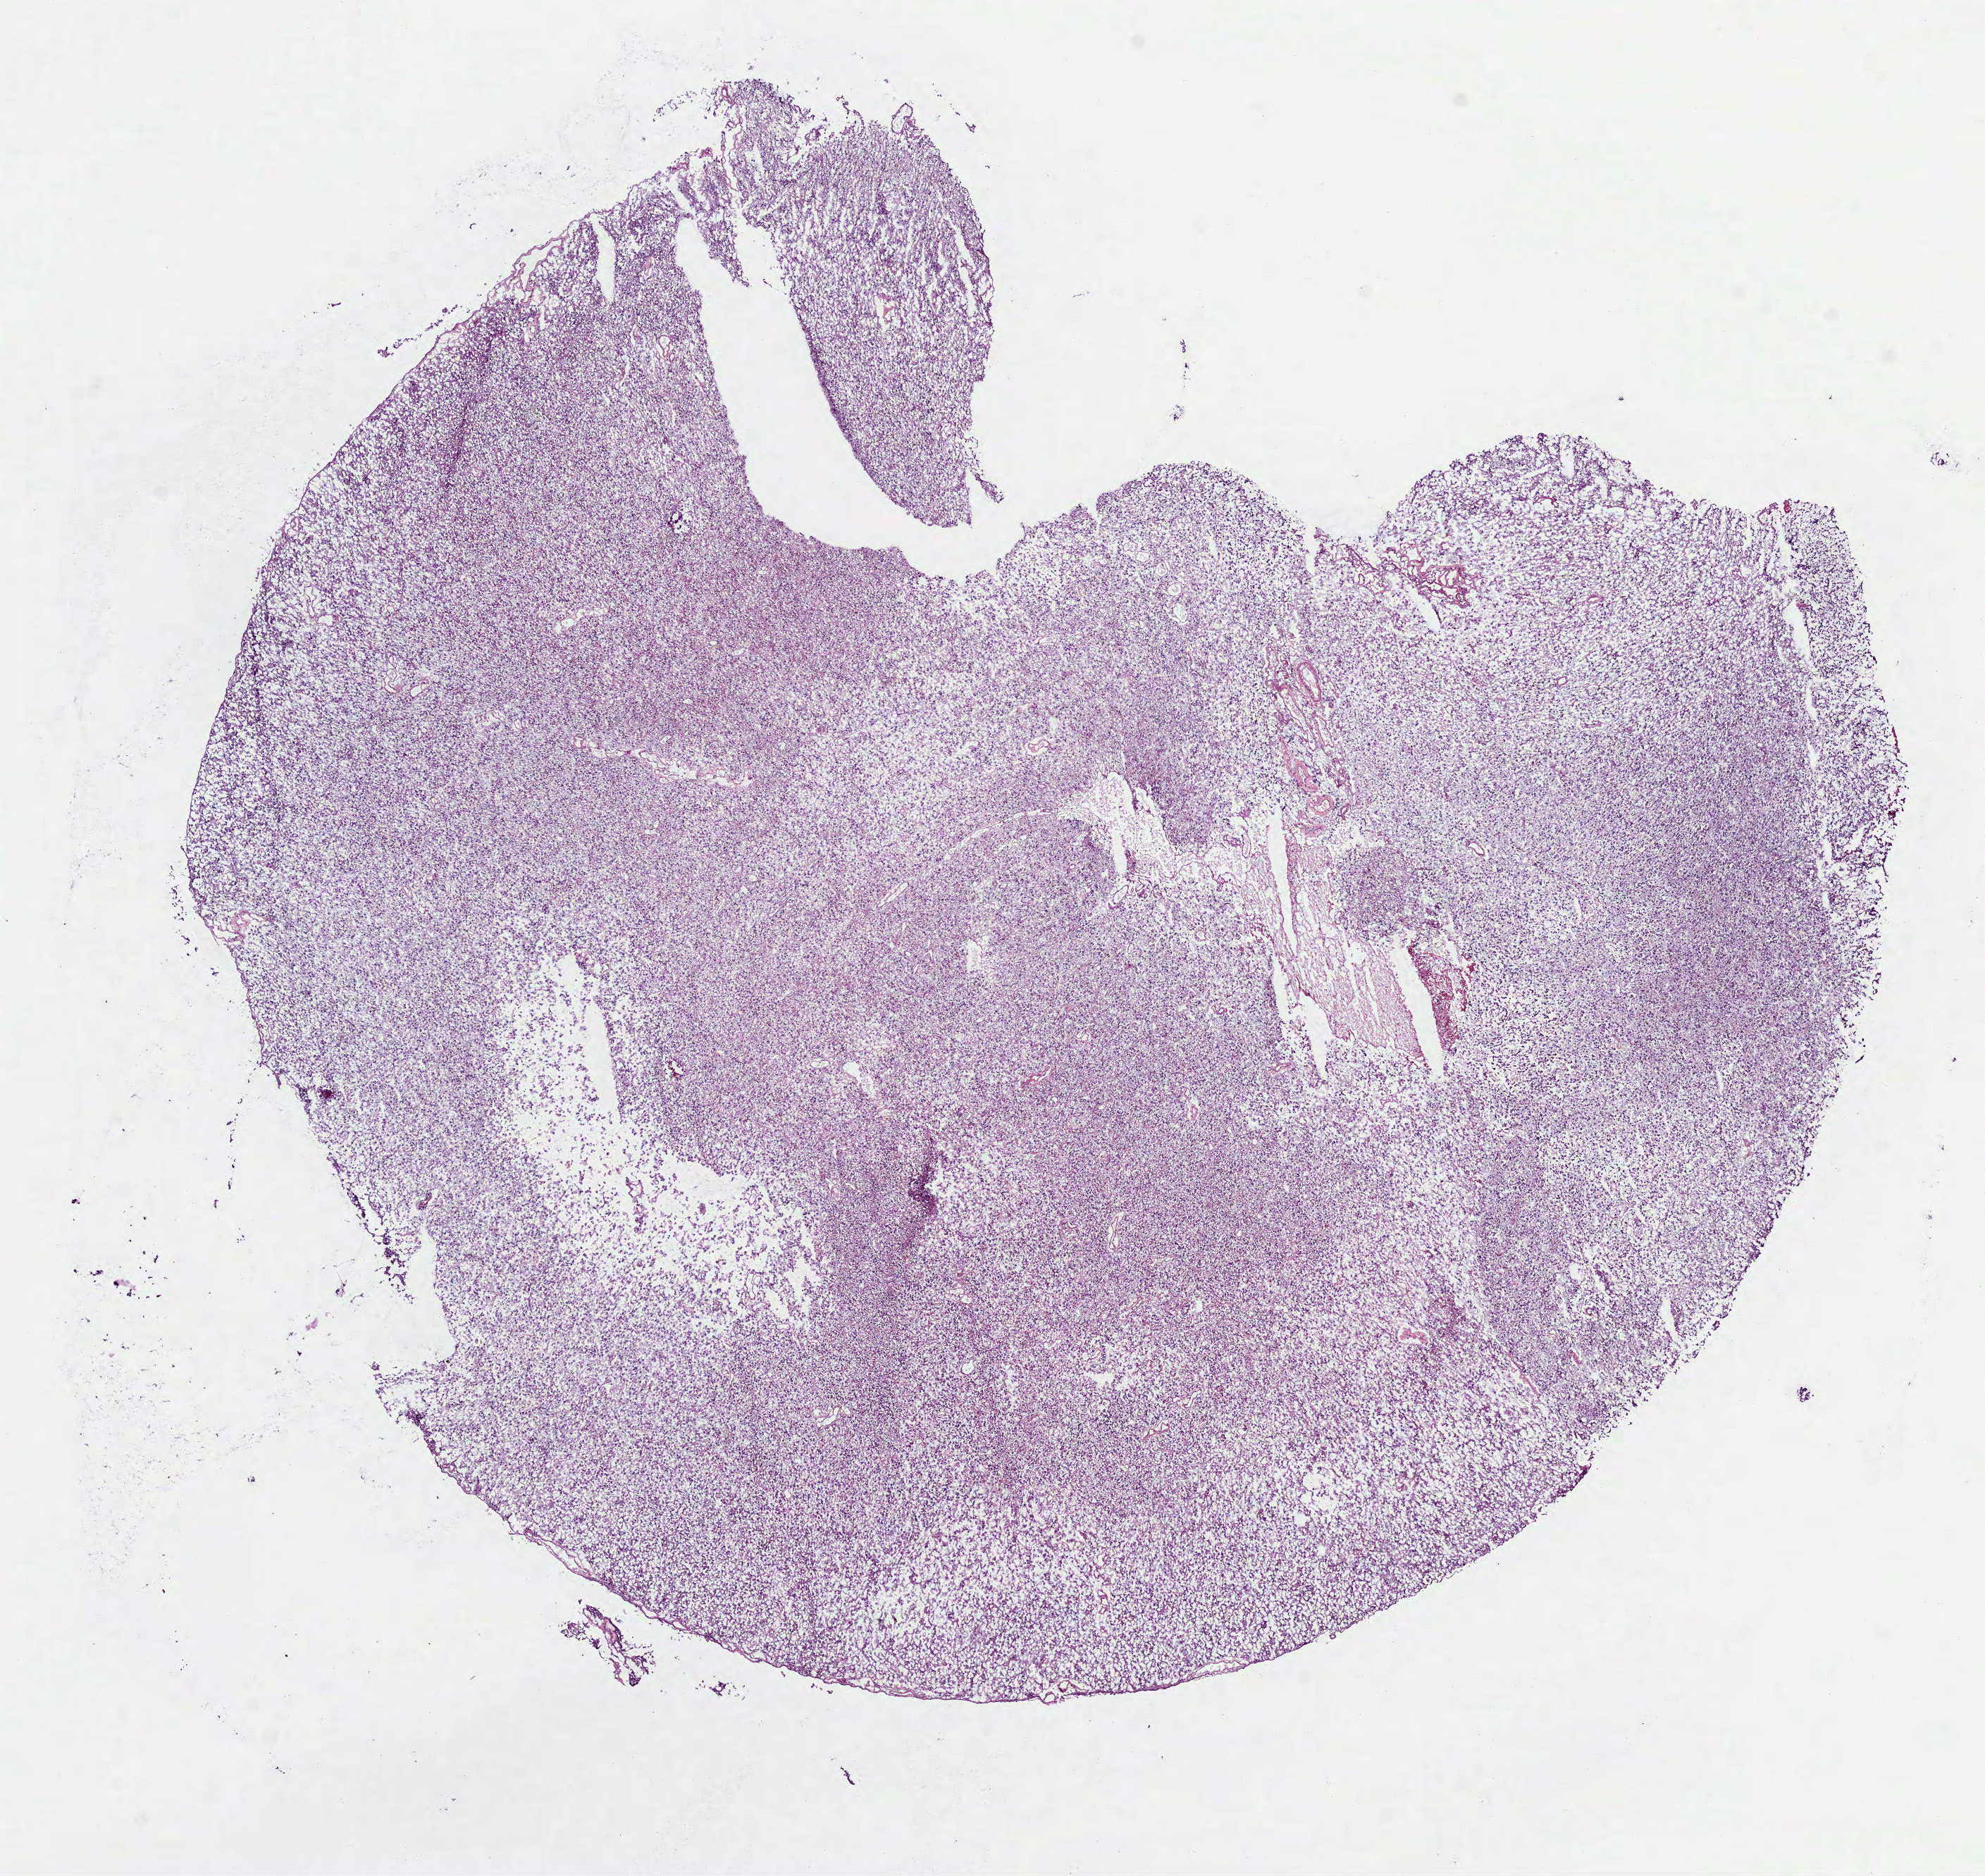
H&E whole-slide image, low-resolution overview of the scanned area, about 11.4 x 10.7 mm, frozen section from the bottom of the tissue portion, primary tumour sample from the brain. Female, age 57 years at initial diagnosis. Histologic grade: G3 (poorly differentiated). Composition of this section per pathologist review: tumour cells 100%, tumour nuclei 80%, normal cells 0%, stromal cells 0%, necrosis 0%.
• histologic diagnosis: Oligodendroglioma, anaplastic
• laterality: right